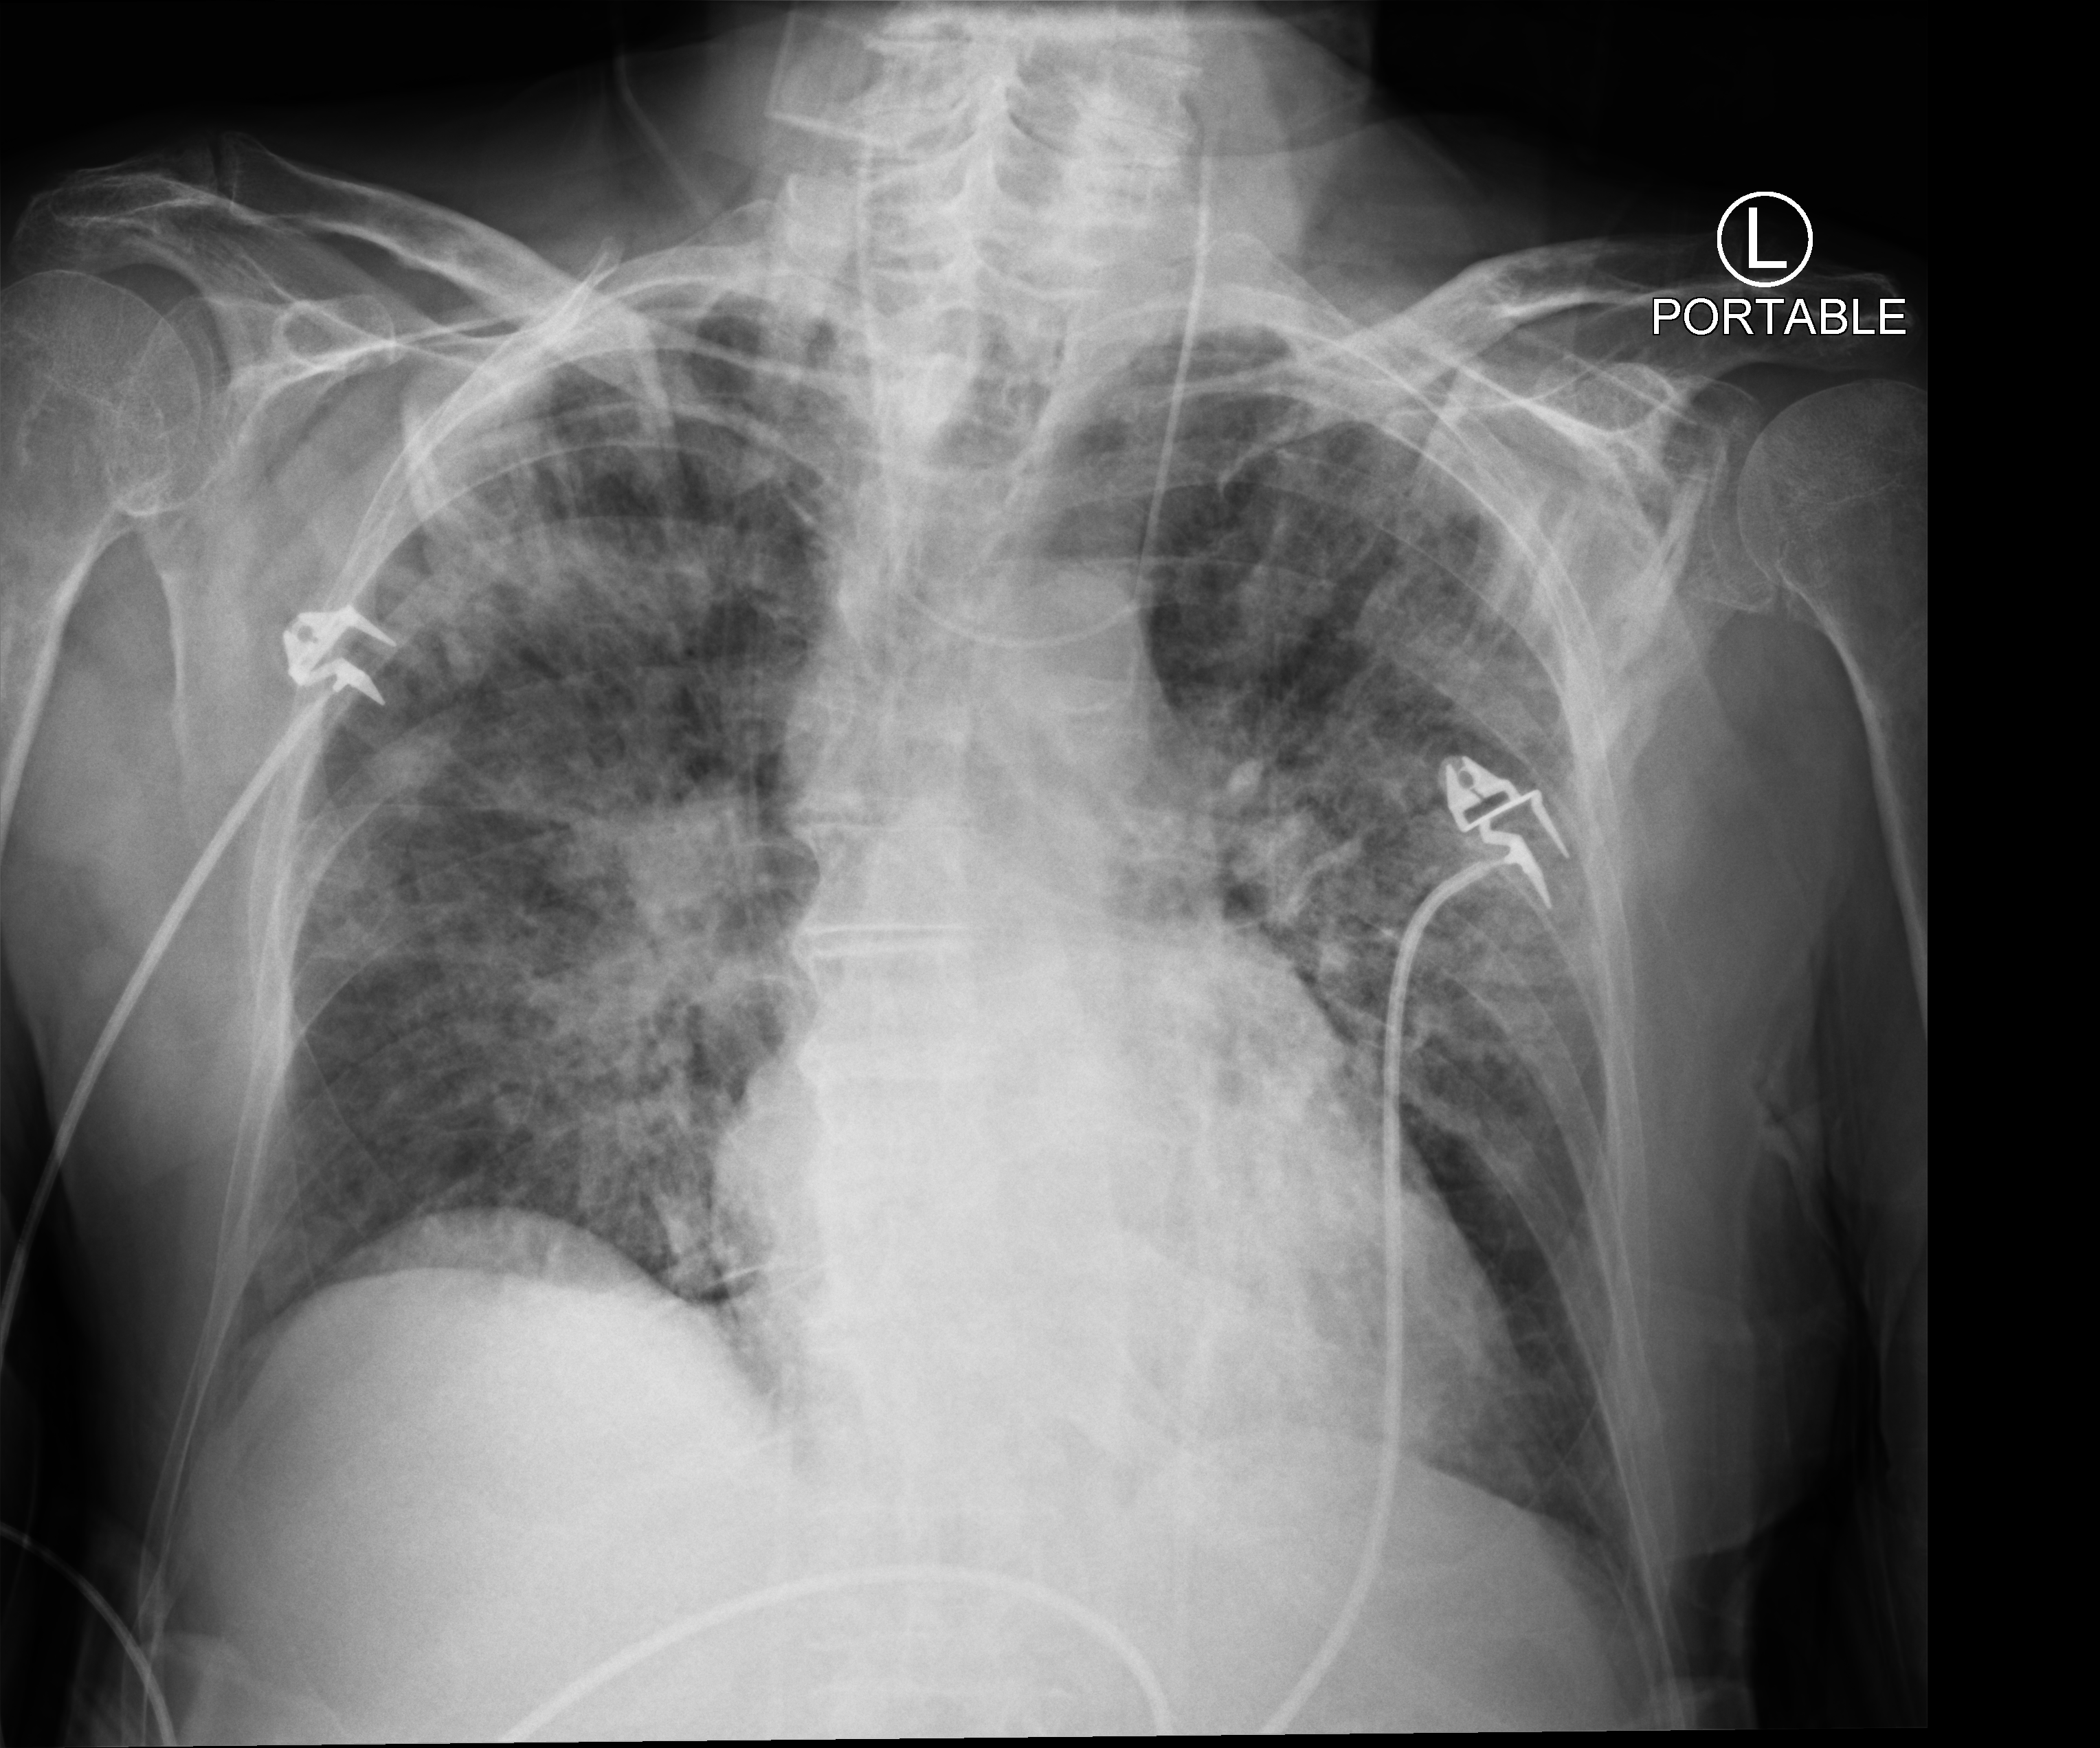
Chest X-ray (portable); anteroposterior (AP) projection. Patient hospitalised with COVID-19; male, aged 75–90 years.
From the hospital-stay record, not from the radiograph (when in the stay this image was taken is not recorded): smoking status (admission record): never.